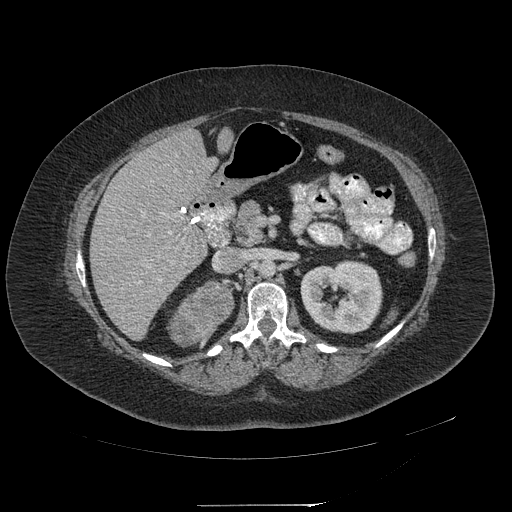
Contrast-enhanced abdominal CT, one axial slice; position 114 of 217 along the scan axis; intravenous contrast given; soft-tissue window (W 400 / L 40 HU); 1.25 mm slice thickness; 512 × 512 image matrix, field of view 453 × 453 mm. Female patient, age 55 years. From the clinical record (not read from this slice): diagnosis: adrenocortical carcinoma; tumour side: right adrenal; tumour size at pathology: 11 cm; Ki-67 index: 20 %; stage (as recorded): 2.
Structures marked on this image (semi-automatic segmentation, software-assisted and operator-edited):
- mass: bounding box (x1, y1, x2, y2) in pixels: (169, 281, 233, 344)